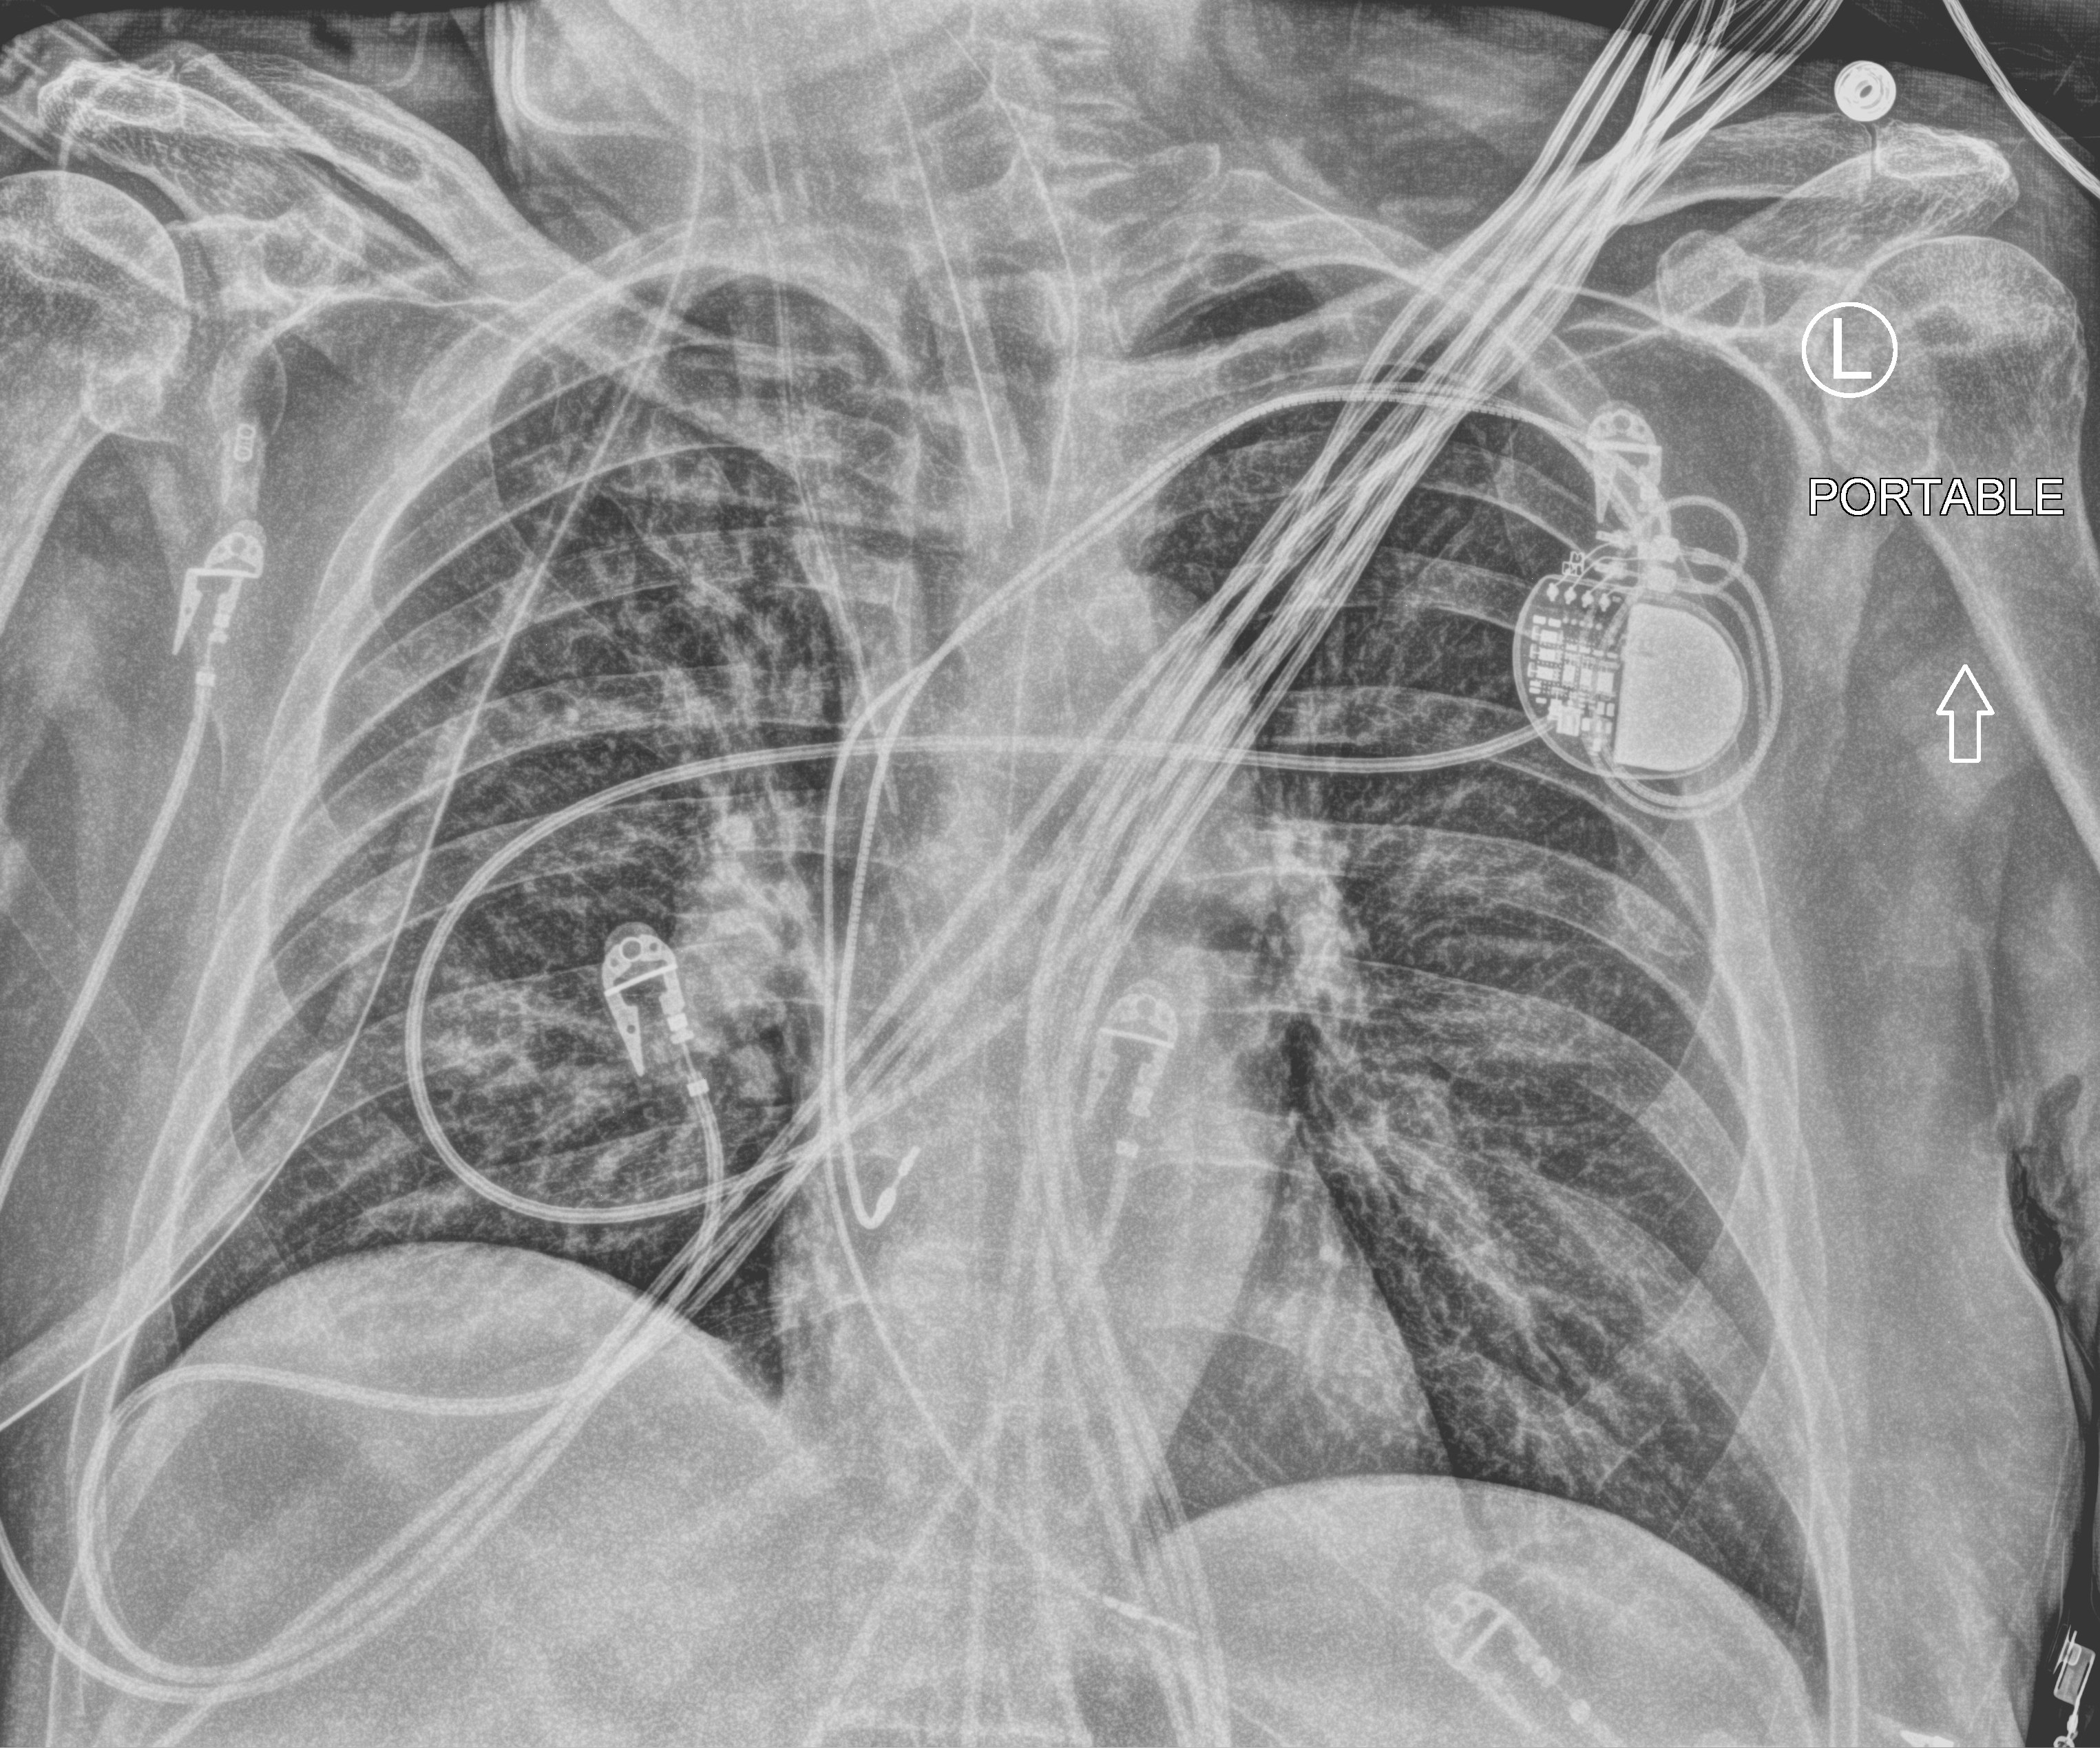
Bedside chest radiograph (computed radiography), anteroposterior (AP) projection. Patient hospitalised with COVID-19; male, aged 60–74 years.
From the hospital-stay record, not from the radiograph (when in the stay this image was taken is not recorded): mechanically ventilated during this hospital stay: no; length of hospital stay: 6 days.